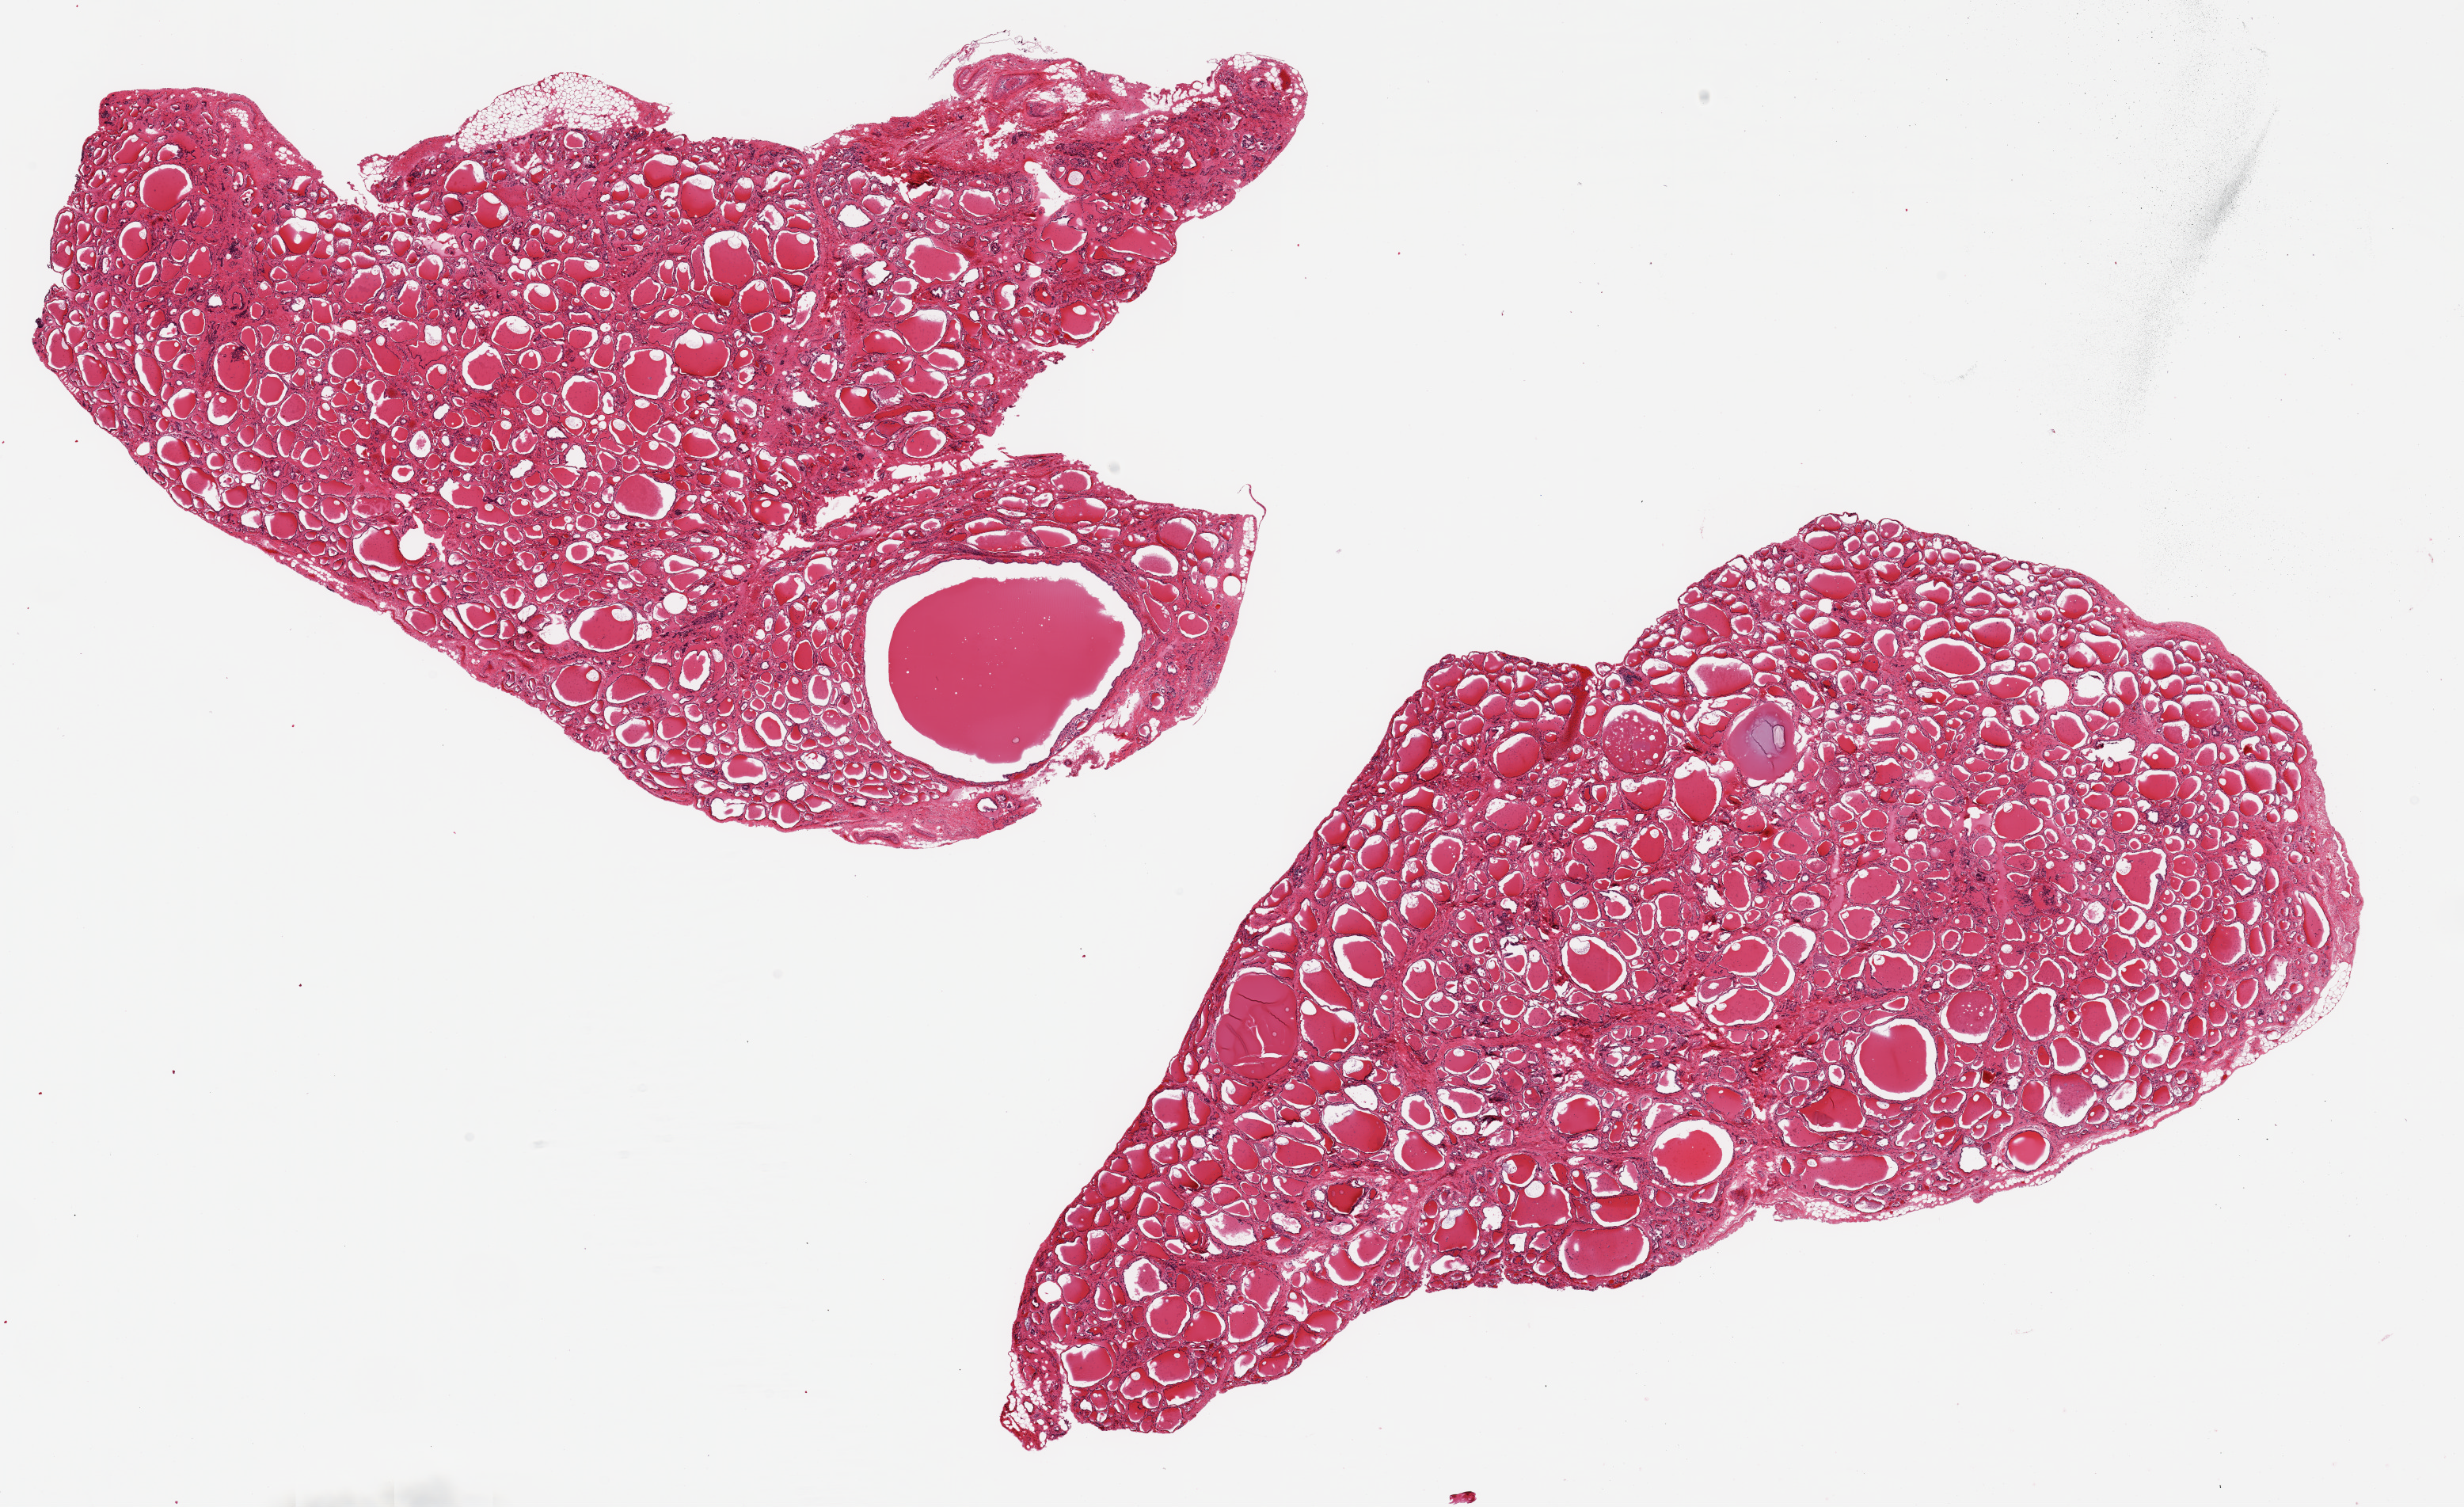
Whole-slide image, H&E stain — shown as a low-resolution overview of the whole scanned area (about 24.6 x 15.0 mm, from a 20x scan). PAXgene-fixed, paraffin-embedded tissue. Sampled site (target tissue): thyroid. Donor tissue sample. Donor: male.
- reviewer comment on this tissue sample: 2 ~12x7mm aliquots. Scattered colloid cysts